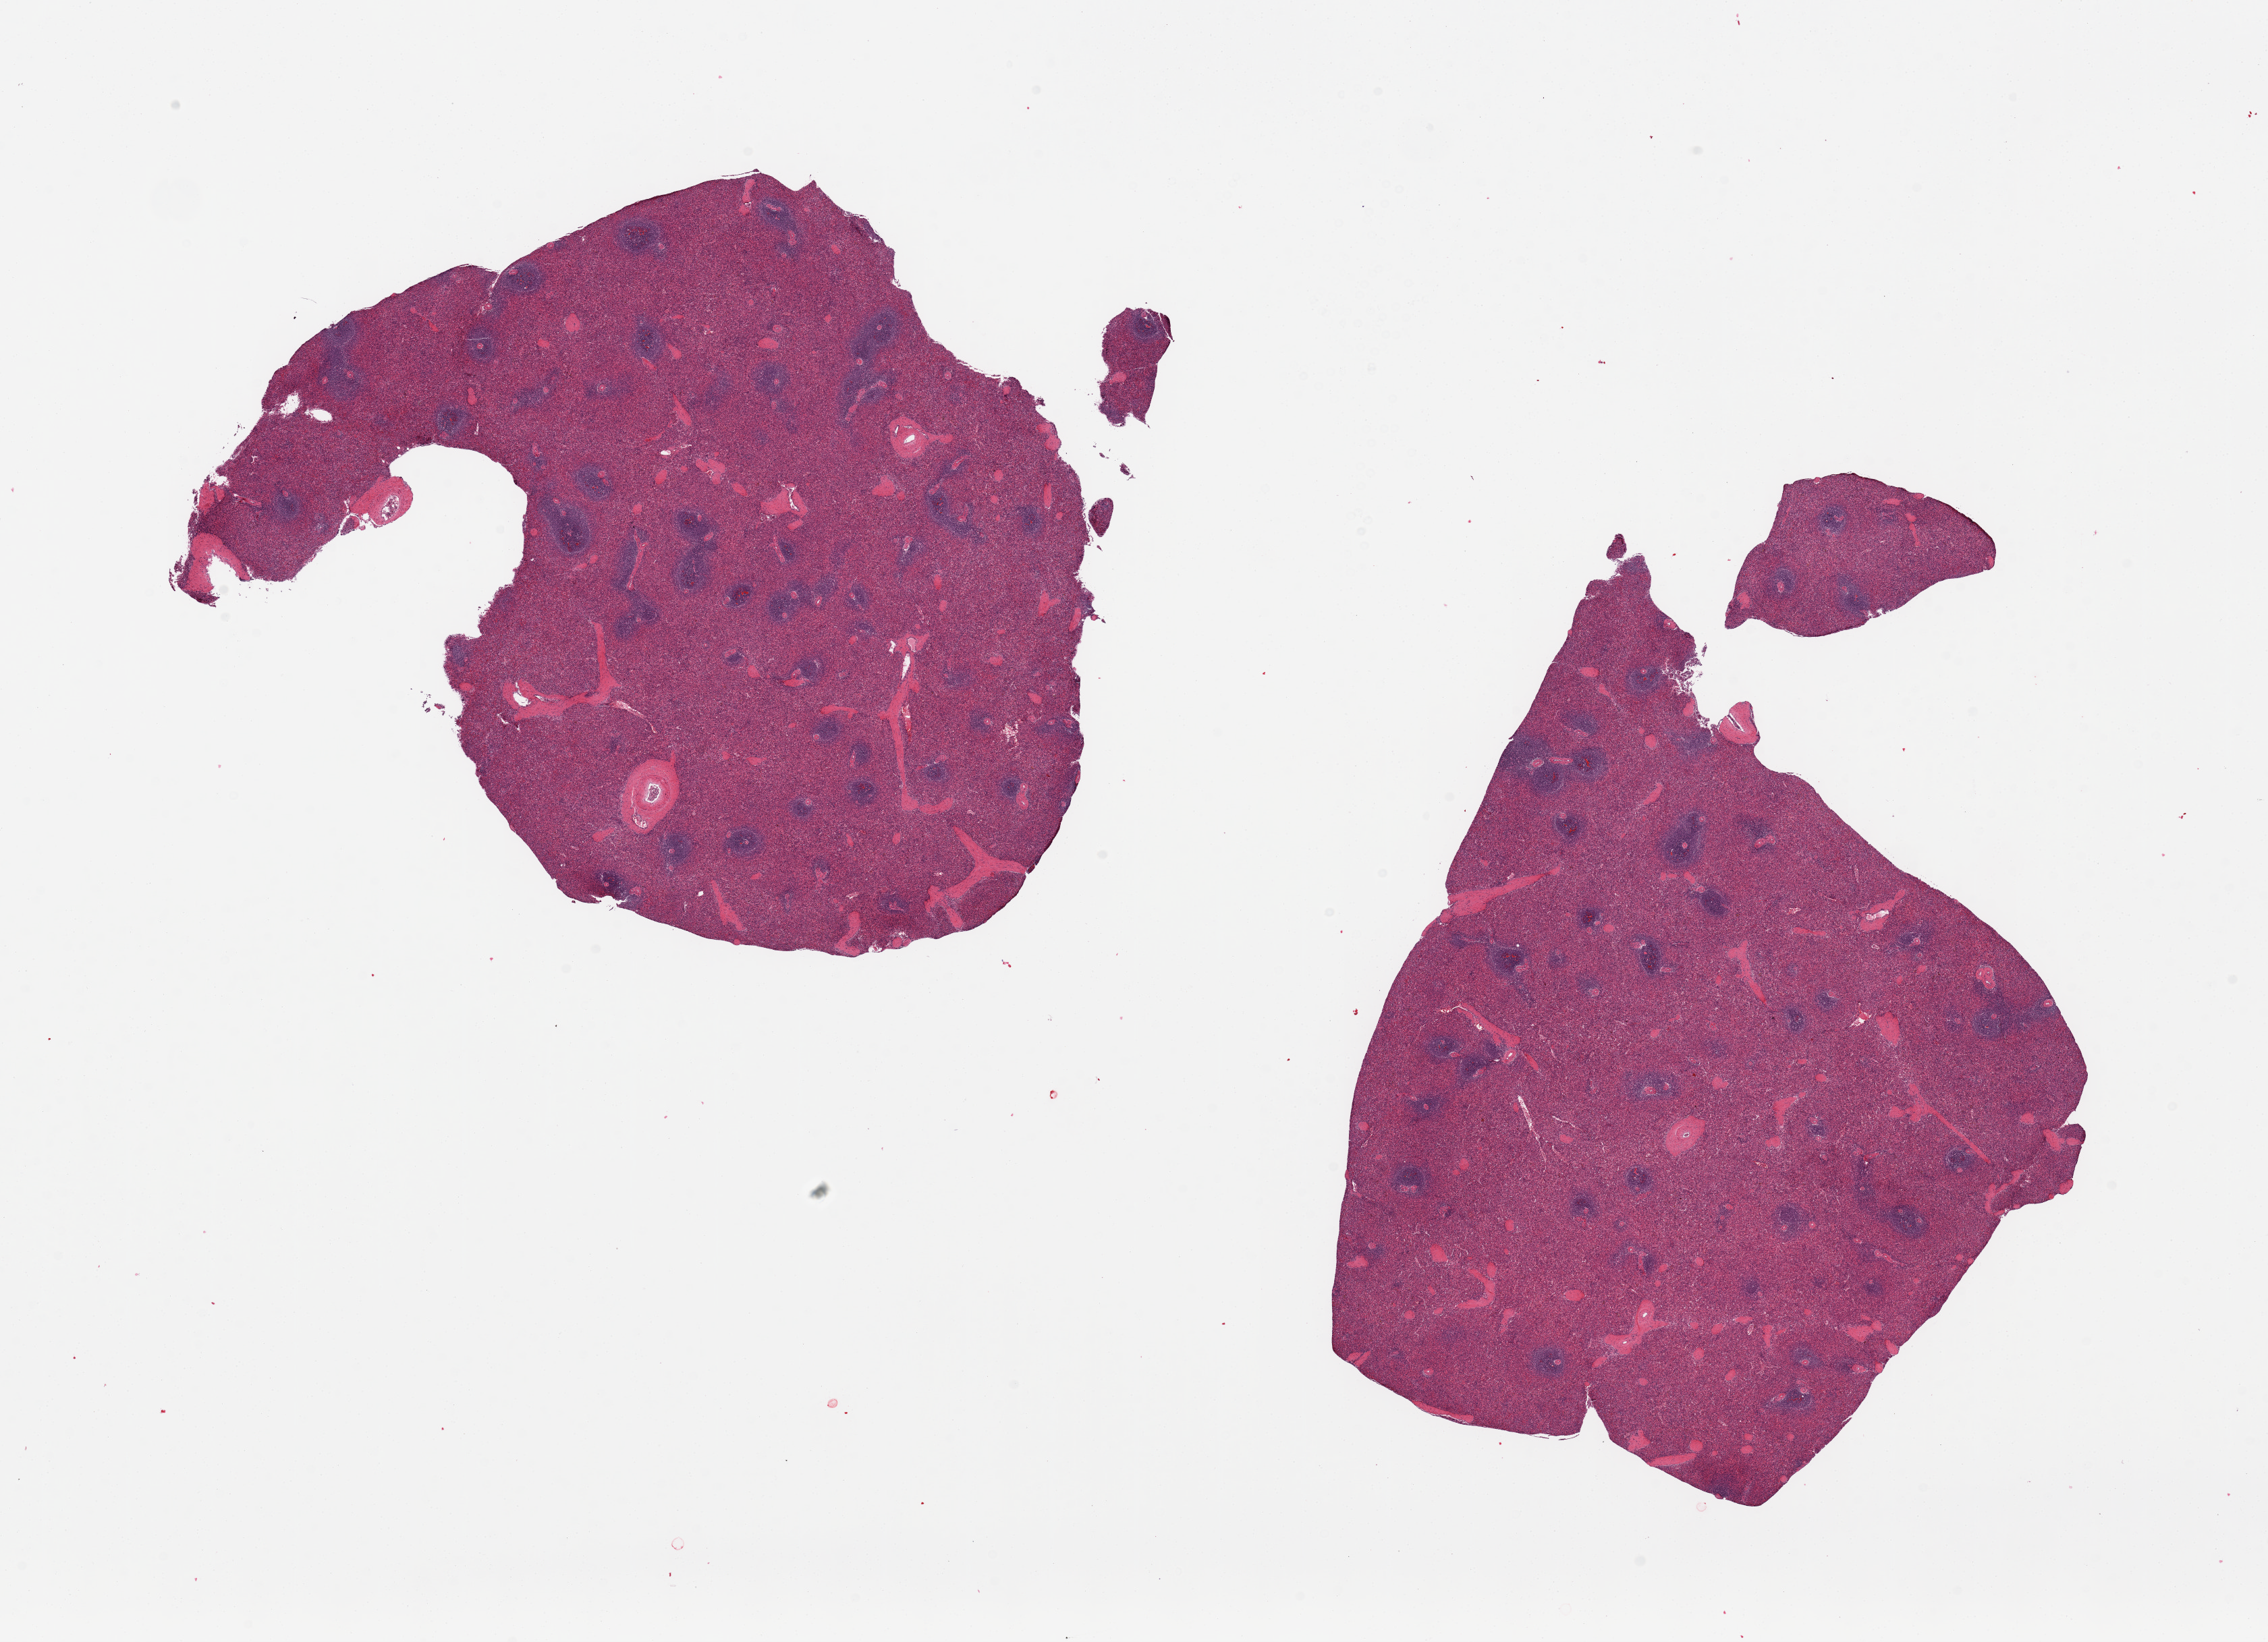
Digitized H&E-stained section, whole scanned area (about 26.6 x 19.2 mm) shown as a low-resolution overview, PAXgene-fixed, paraffin-embedded tissue, target tissue: spleen, tissue donor sample. Donor sex: male.
* pathologist's review note for this sample: 2 pieces, well-preserved; no abnormalities